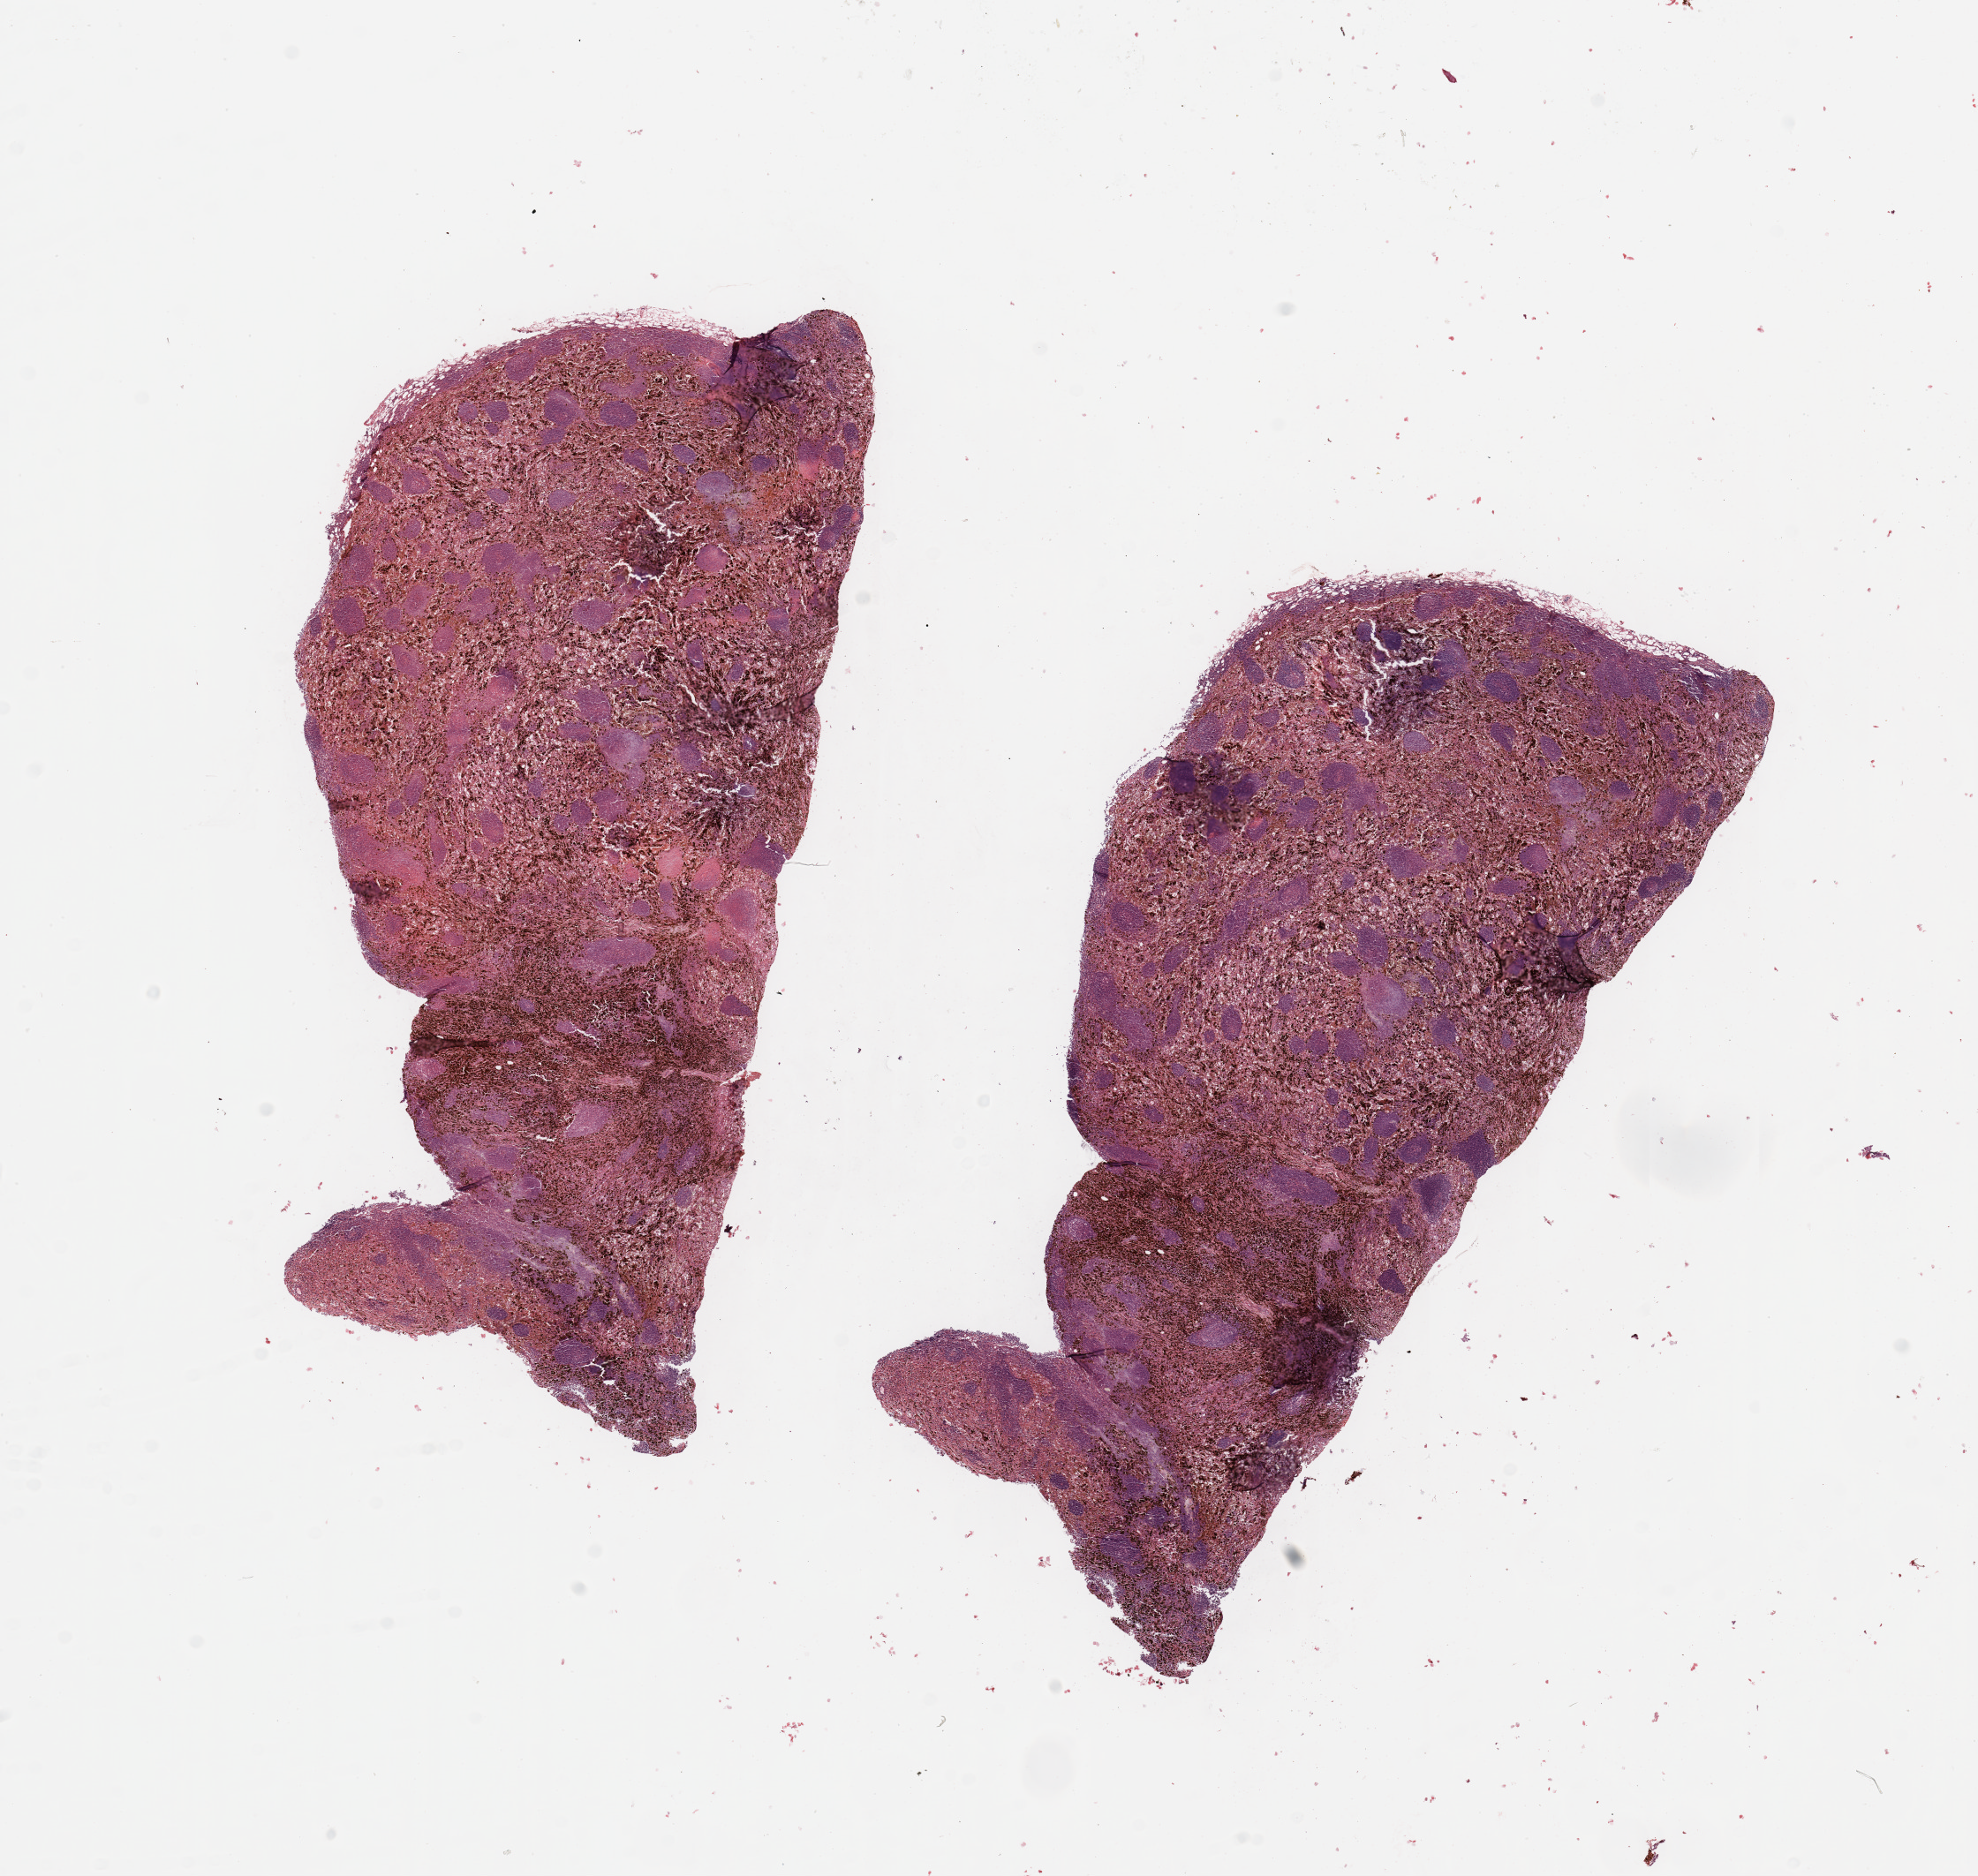
Digitized Hematoxylin and eosin (H&E) stained tissue section (whole slide), low-resolution overview of the scanned area, about 17.7 x 16.8 mm (acquisition: 20x scan); melanoma tumour tissue; sampled site not recorded. Patient: male, age 74 years.
Primary tumour site (as recorded): palms and soles. Patient diagnosis (cohort enrolment): cutaneous melanoma (skin).